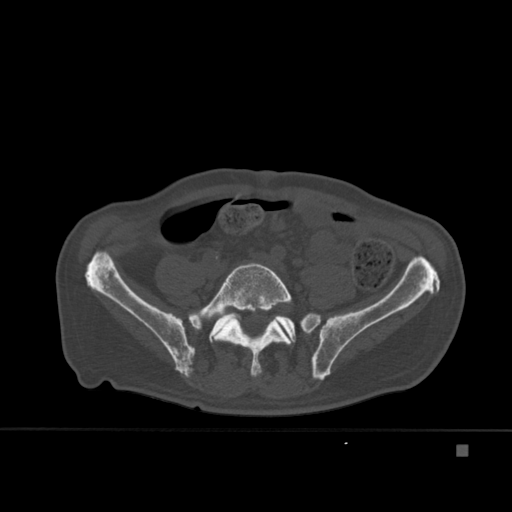
CT including the spine, one axial slice. Slice 101 of 451 in the series (ordered by position). Bone window (W 1800 / L 400 HU). 512 × 512 image matrix, field of view 378 × 378 mm. Patient: male, 75 years. From the clinical record (not read from this slice): primary cancer: prostate.
Annotated regions visible in this slice (semi-automatic segmentation, software-assisted and operator-edited):
- L5 vertebra: box from (x=188, y=263) to (x=292, y=377) px
- T7 vertebra: (x=213, y=295)–(x=246, y=335)